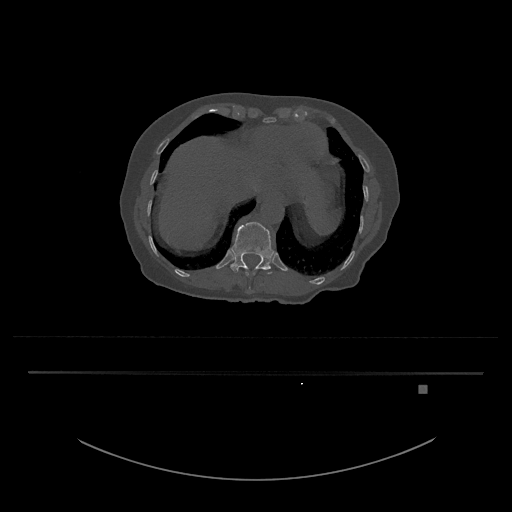
CT including the spine, one axial slice. Slice 628 of 797 in the series (ordered by position). Reconstruction kernel Br40s/3. 120 kVp. Bone window (W 1800 / L 400 HU). 0.5 mm slice thickness. 512 × 512 image matrix. Patient: female, 57 years. Case-level facts recorded for this patient, not image findings: primary cancer: cervical.
Annotated regions visible in this slice (semi-automatically segmented with operator editing):
- T11 vertebra: bounding box (x1, y1, x2, y2) in pixels: (246, 272, 255, 276)
- T12 vertebra: (230, 222, 275, 274)